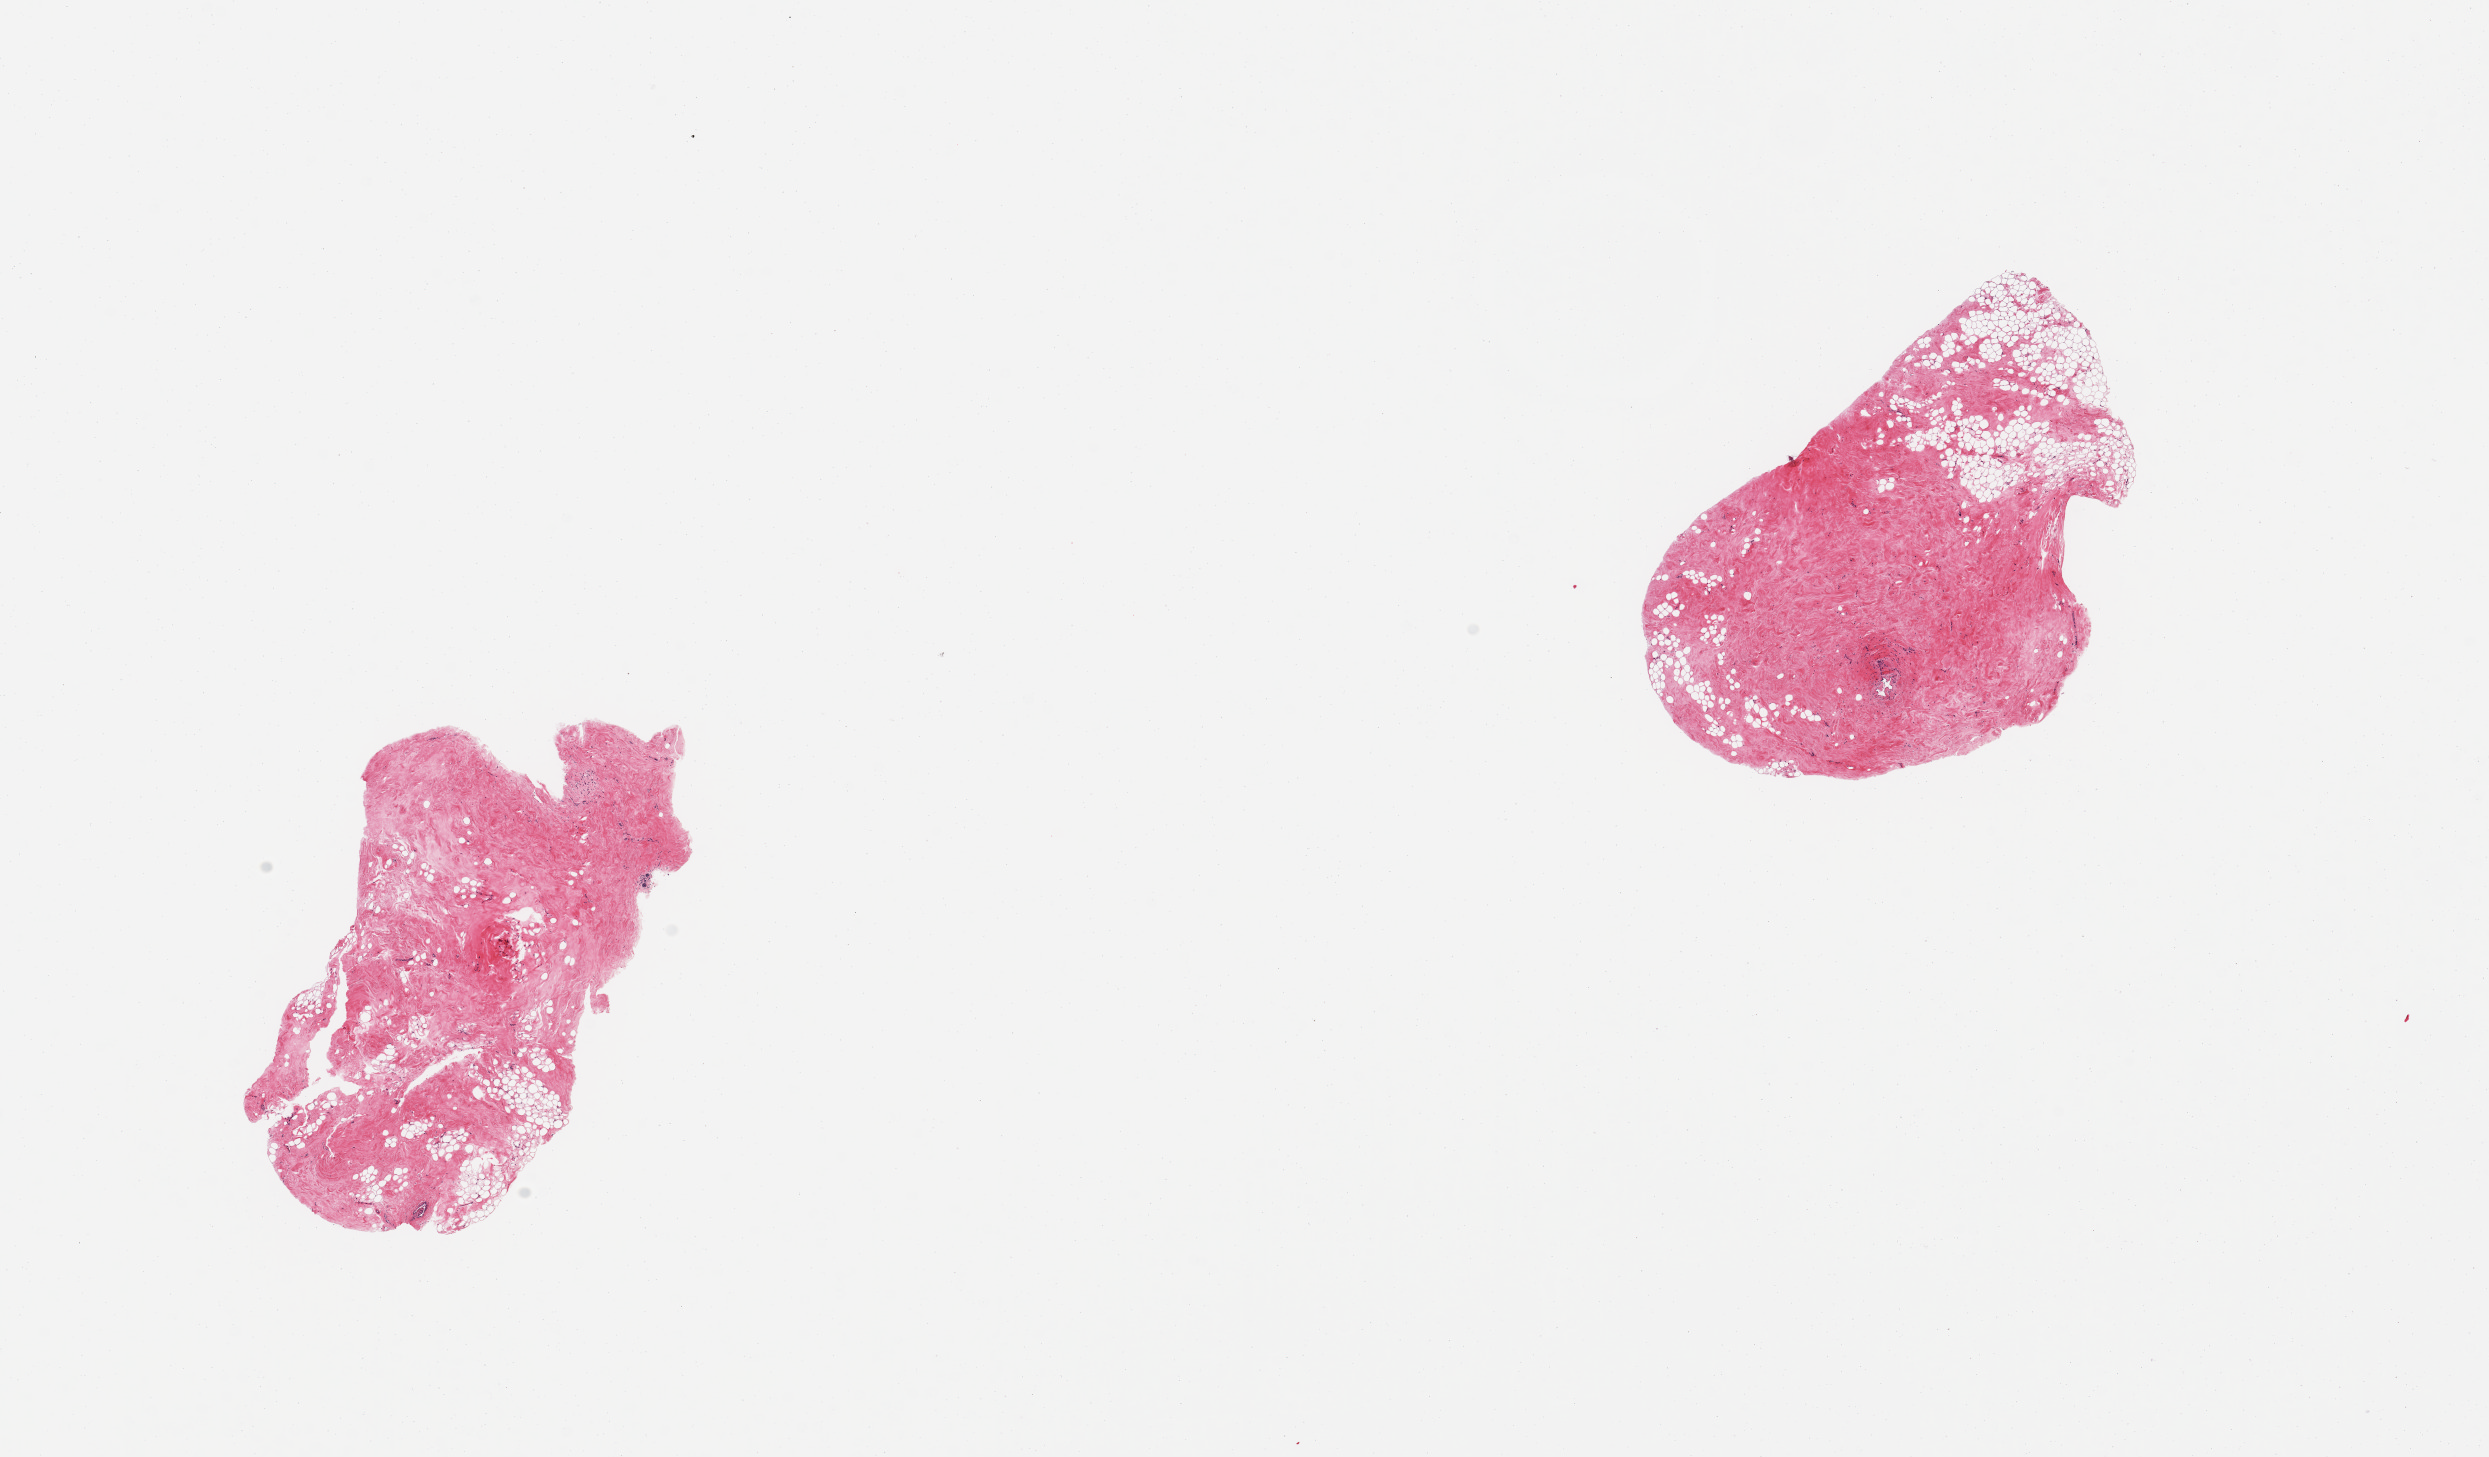
Whole-slide image, H&E stain, low-resolution overview of the scanned area, about 19.7 x 11.5 mm (acquisition: 20x scan); PAXgene-fixed, paraffin-embedded tissue; section of breast (target tissue); donor tissue sample. Donor sex: female.
Reviewer comment on this tissue sample: 2 pieces; dense fibrocollagenous tissue with smaller component of fat.